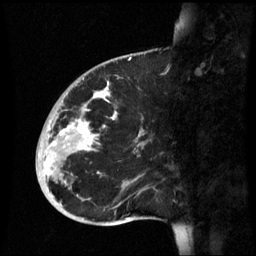
Breast MRI (dynamic contrast-enhanced), one sagittal slice; slice 21 of 60 in the series (ordered by position); dynamic contrast-enhanced series, image 2 of 3 at this slice position (ordered by acquisition); 1.5 T; TE 4.2 ms, TR 8.9 ms; 2.6 mm slice thickness; 256 × 256 image matrix. Patient: female, 35 years. From the clinical record (not read from this slice): setting: breast cancer imaged before/during neoadjuvant chemotherapy; receptor status: HR-positive, HER2-negative.
Annotated regions visible in this slice (semi-automatic segmentation, software-assisted and operator-edited):
- analysis volume of interest (the breast-tissue region the enhancement analysis was run in; not a lesion): bounding box <36,74,163,221> (left, top, right, bottom; pixels)
- tumour enhancement mask (voxels above the 70 % enhancement threshold inside the analysis volume of interest): <44,82,116,175>